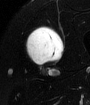
MRI of an extremity soft-tissue mass, one axial slice. Position 43 of 65 along the scan axis. T2-weighted fat-saturated. MR volume resampled by the dataset authors to the PET/CT grid (not the native acquisition matrix). 90 × 105 image matrix. Male patient. From the clinical record (not read from this slice): histological type: mixoid liposarcoma; grade: low; site of the primary tumour: left thigh.
Structures marked on this image (expert contour drawn on MRI and transferred to this co-registered scan by the dataset authors):
- gross tumour volume (mass): bounding box (x1, y1, x2, y2) in pixels: (23, 27, 63, 67)